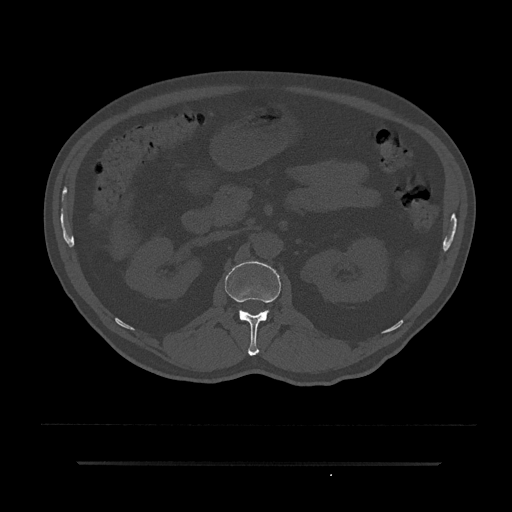
CT including the spine, one axial slice; slice 132 of 797 in the series (ordered by position); reconstruction kernel Br40s/3; 120 kVp; bone window (W 1800 / L 400 HU); 0.5 mm slice thickness; 512 × 512 image matrix, field of view 464 × 464 mm. Patient: male, 59 years. Case-level facts recorded for this patient, not image findings: primary cancer: bile ducts.
Structures marked on this image (semi-automatic segmentation, software-assisted and operator-edited):
- L1 vertebra: bounding box <225,261,281,356> (left, top, right, bottom; pixels)